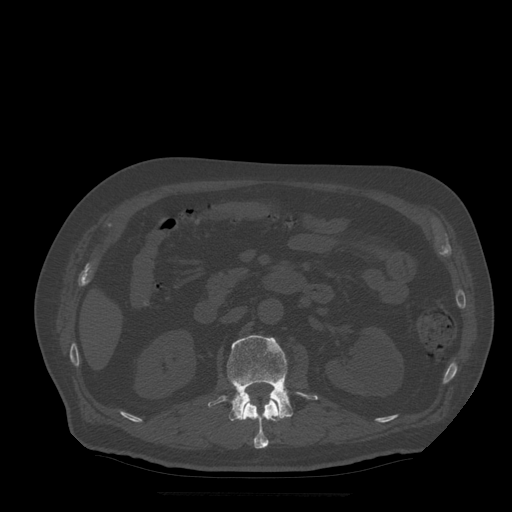
CT including the spine, one axial slice. Position 178 of 522 along the scan axis. Bone window (W 1800 / L 400 HU). 1.25 mm slice thickness. 512 × 512 image matrix, field of view 420 × 420 mm. Patient age 72 years. Case-level facts recorded for this patient, not image findings: primary cancer: prostate.
Annotated regions visible in this slice (semi-automatically segmented with operator editing):
- L1 vertebra: bounding box <242,397,281,449> (left, top, right, bottom; pixels)
- L2 vertebra: <208,336,318,421>